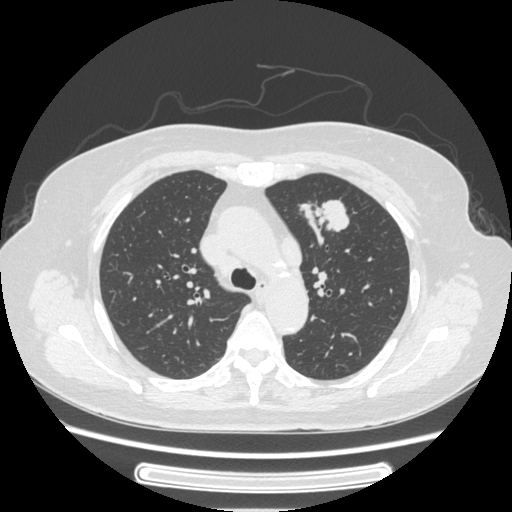
Chest CT, one axial slice. Slice 169 of 227 in the series (ordered by position). Reconstruction kernel STANDARD. 120 kVp. Lung window (W 1500 / L -600 HU). 512 × 512 image matrix, field of view 363 × 363 mm. Female patient, age 77 years. Case-level facts recorded for this patient, not image findings: clinical TNM (as recorded): T1c N3 M0.
Outlined on this slice (bounding box drawn by a radiologist):
- lung tumour (recorded histology: adenocarcinoma): bounding box [x1, y1, x2, y2] px = [299, 192, 357, 253]